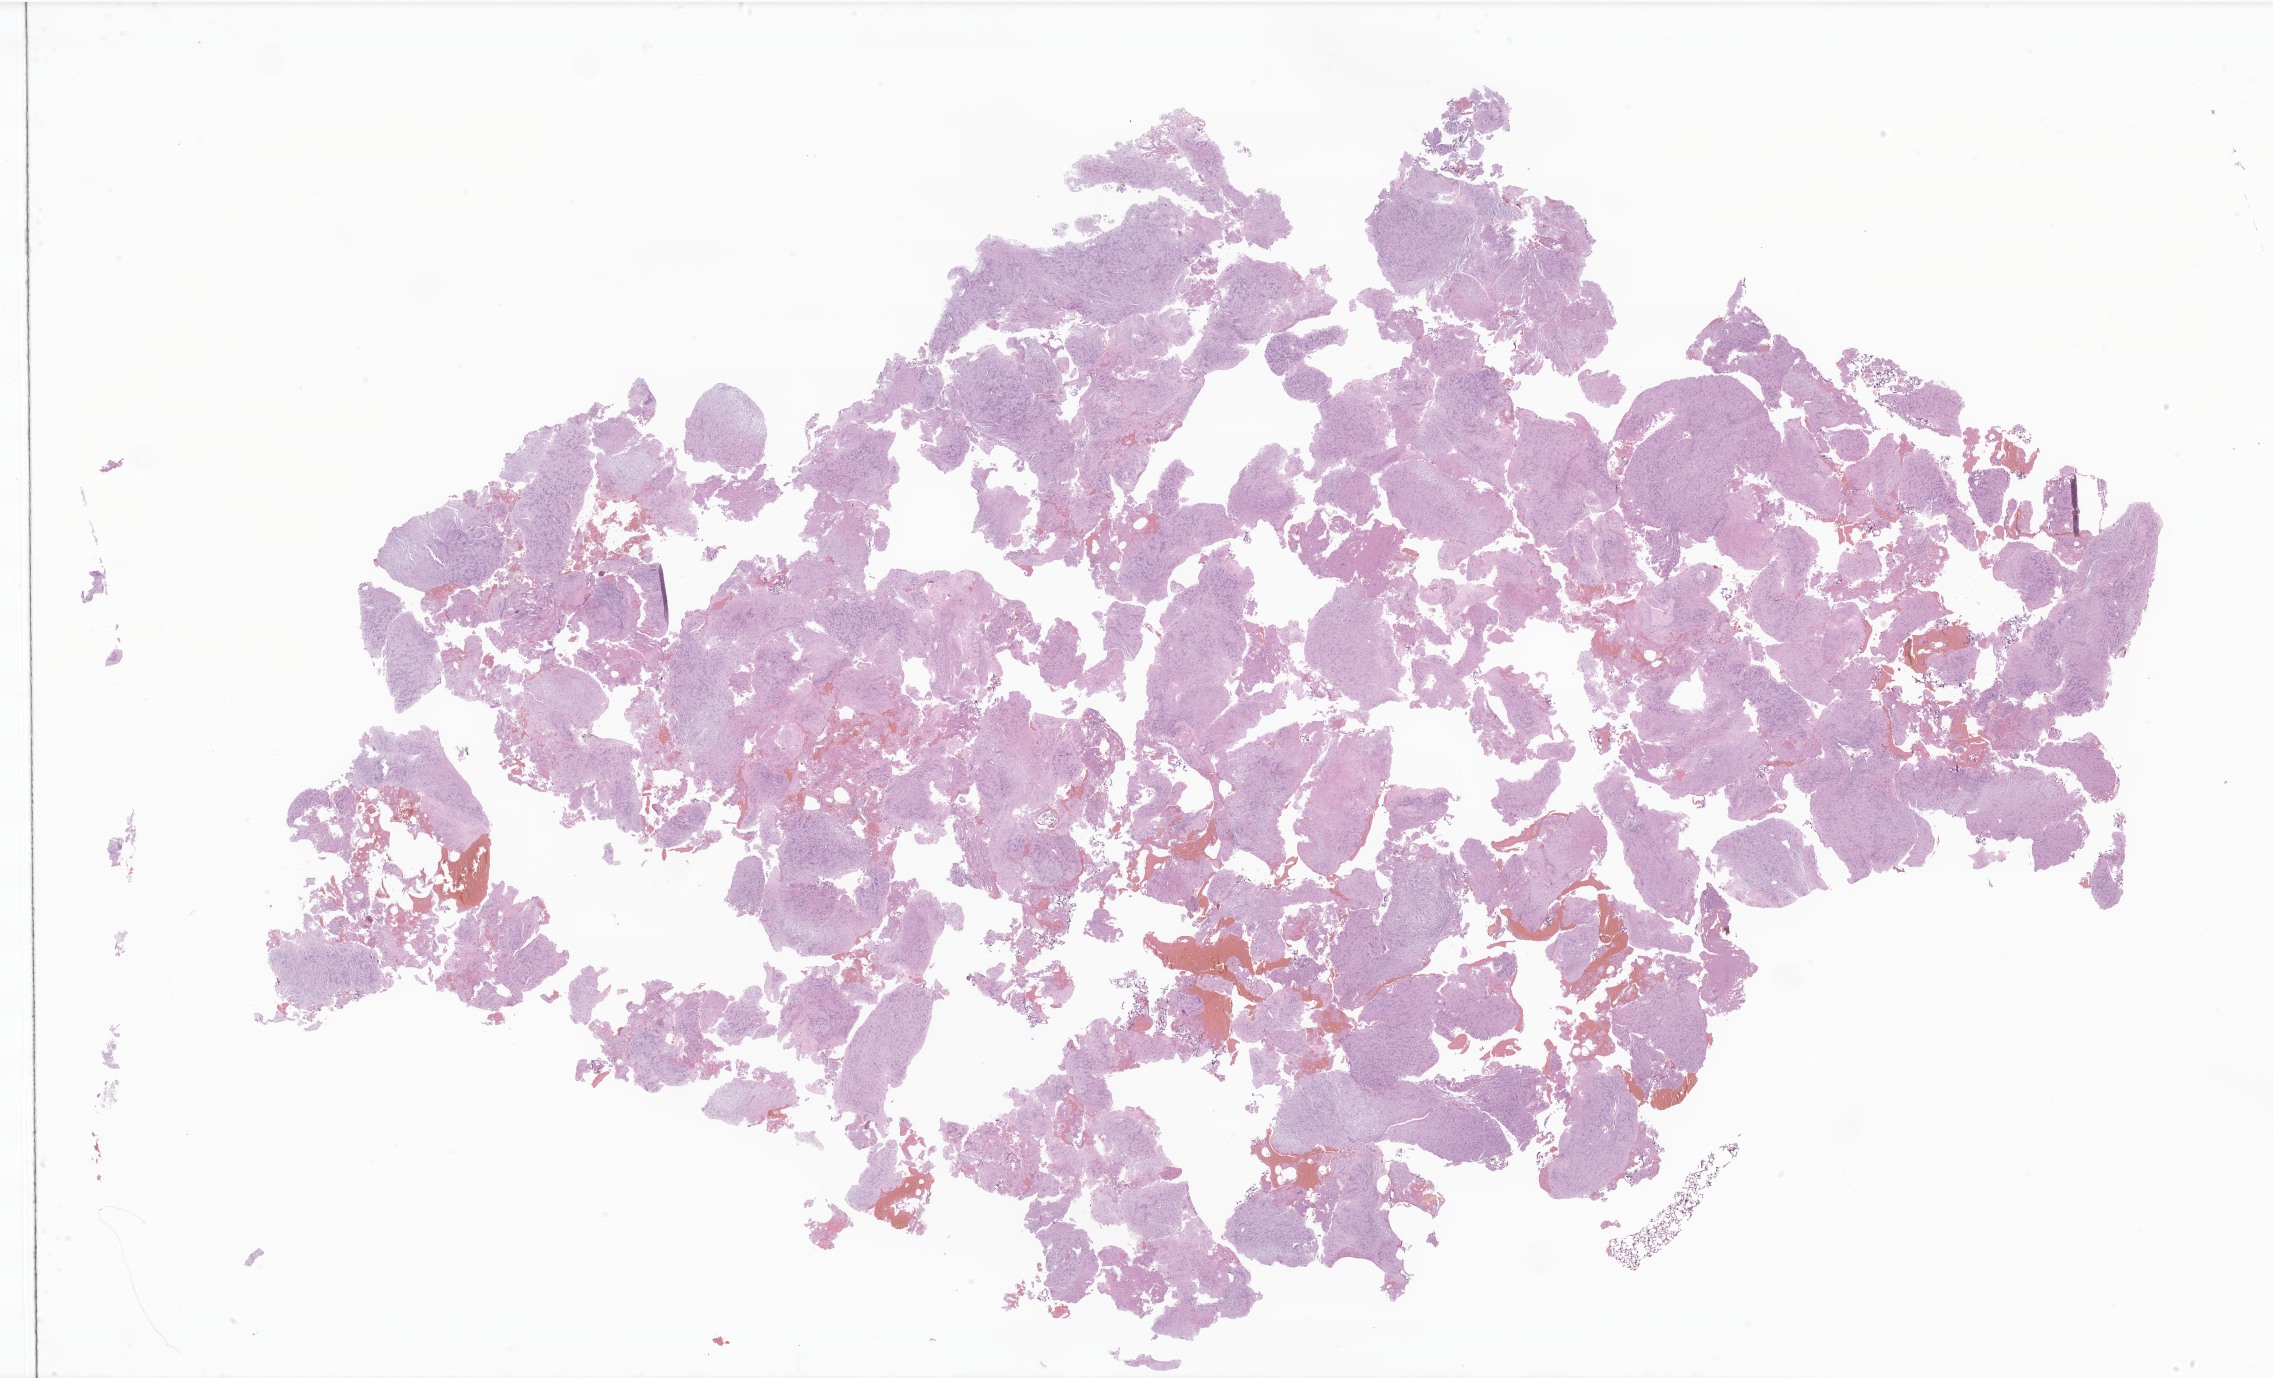
H&E whole-slide image of tumor tissue from the nervous system — whole scanned area (about 38.3 x 23.2 mm) shown as a low-resolution overview, FFPE section. Patient female; age 179 months (14 years 11 months).
Diagnosis: Schwannoma, NOS.